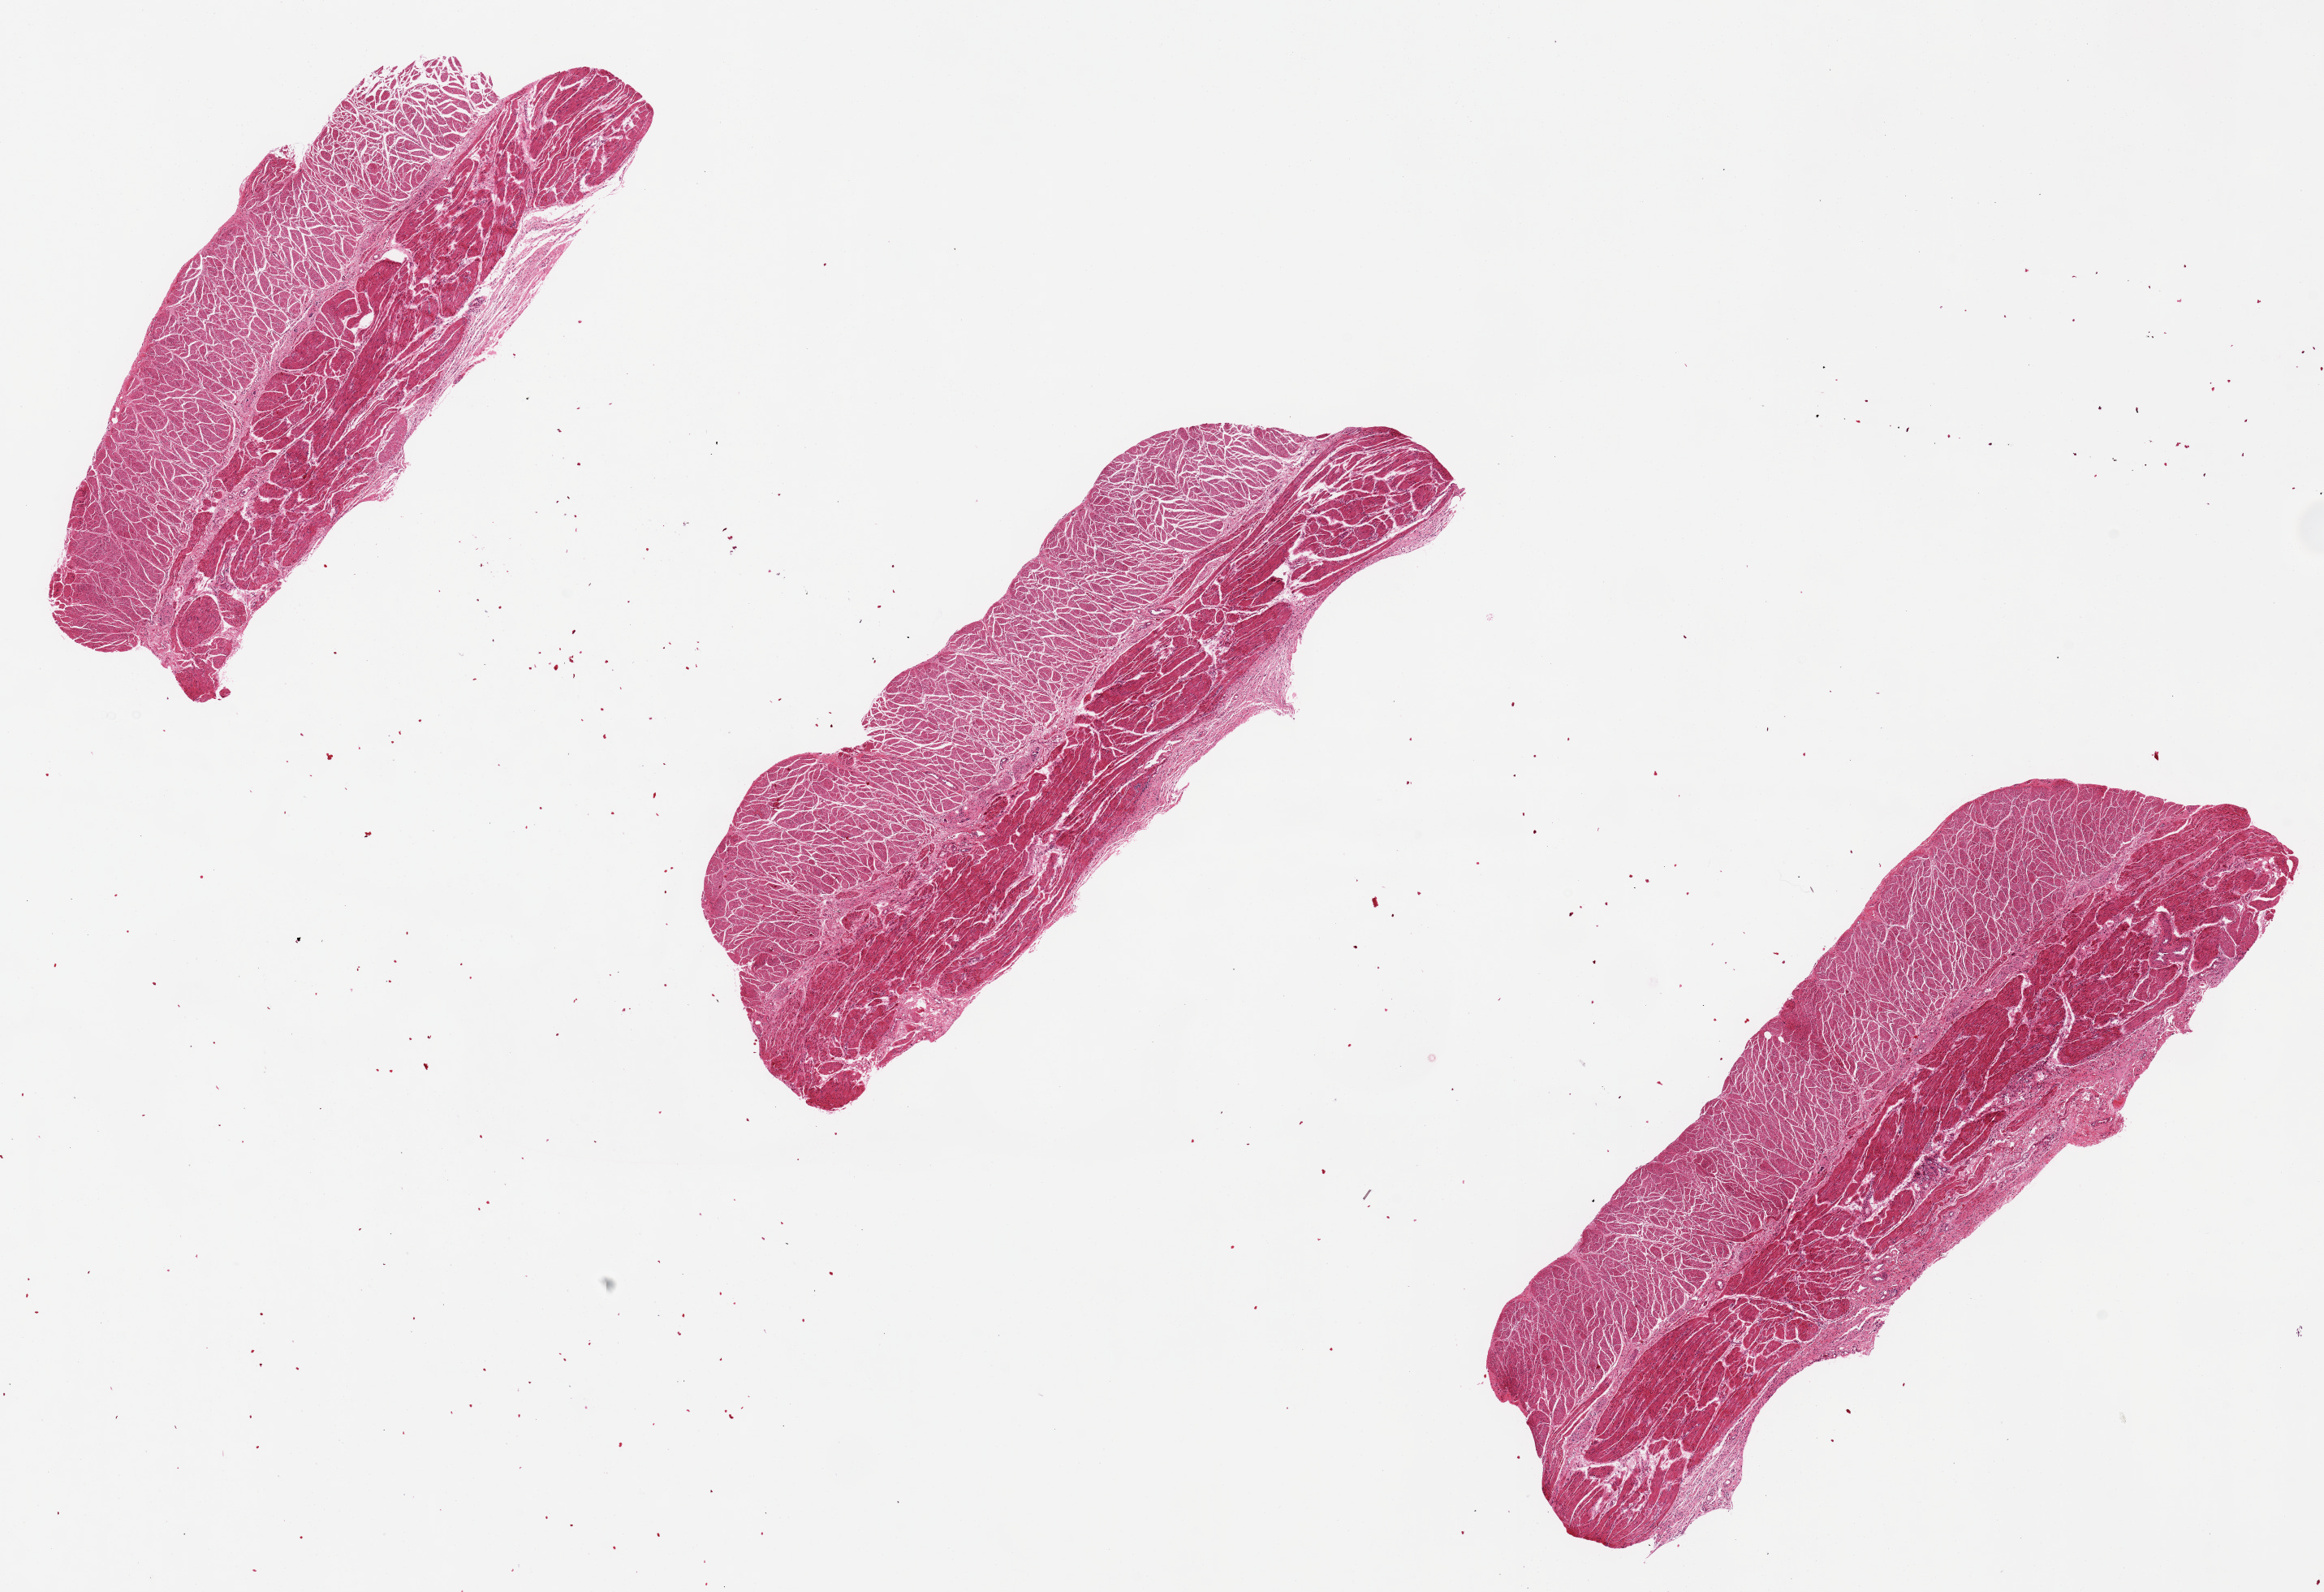
H&E whole-slide image, brightfield, whole scanned area (about 22.6 x 15.5 mm) shown as a low-resolution overview, PAXgene-fixed paraffin-embedded (PFPE) section, target tissue: esophageal muscle, tissue donor sample. Donor: female.
* reviewer comment on this tissue sample: Muscularis only; no mucosa